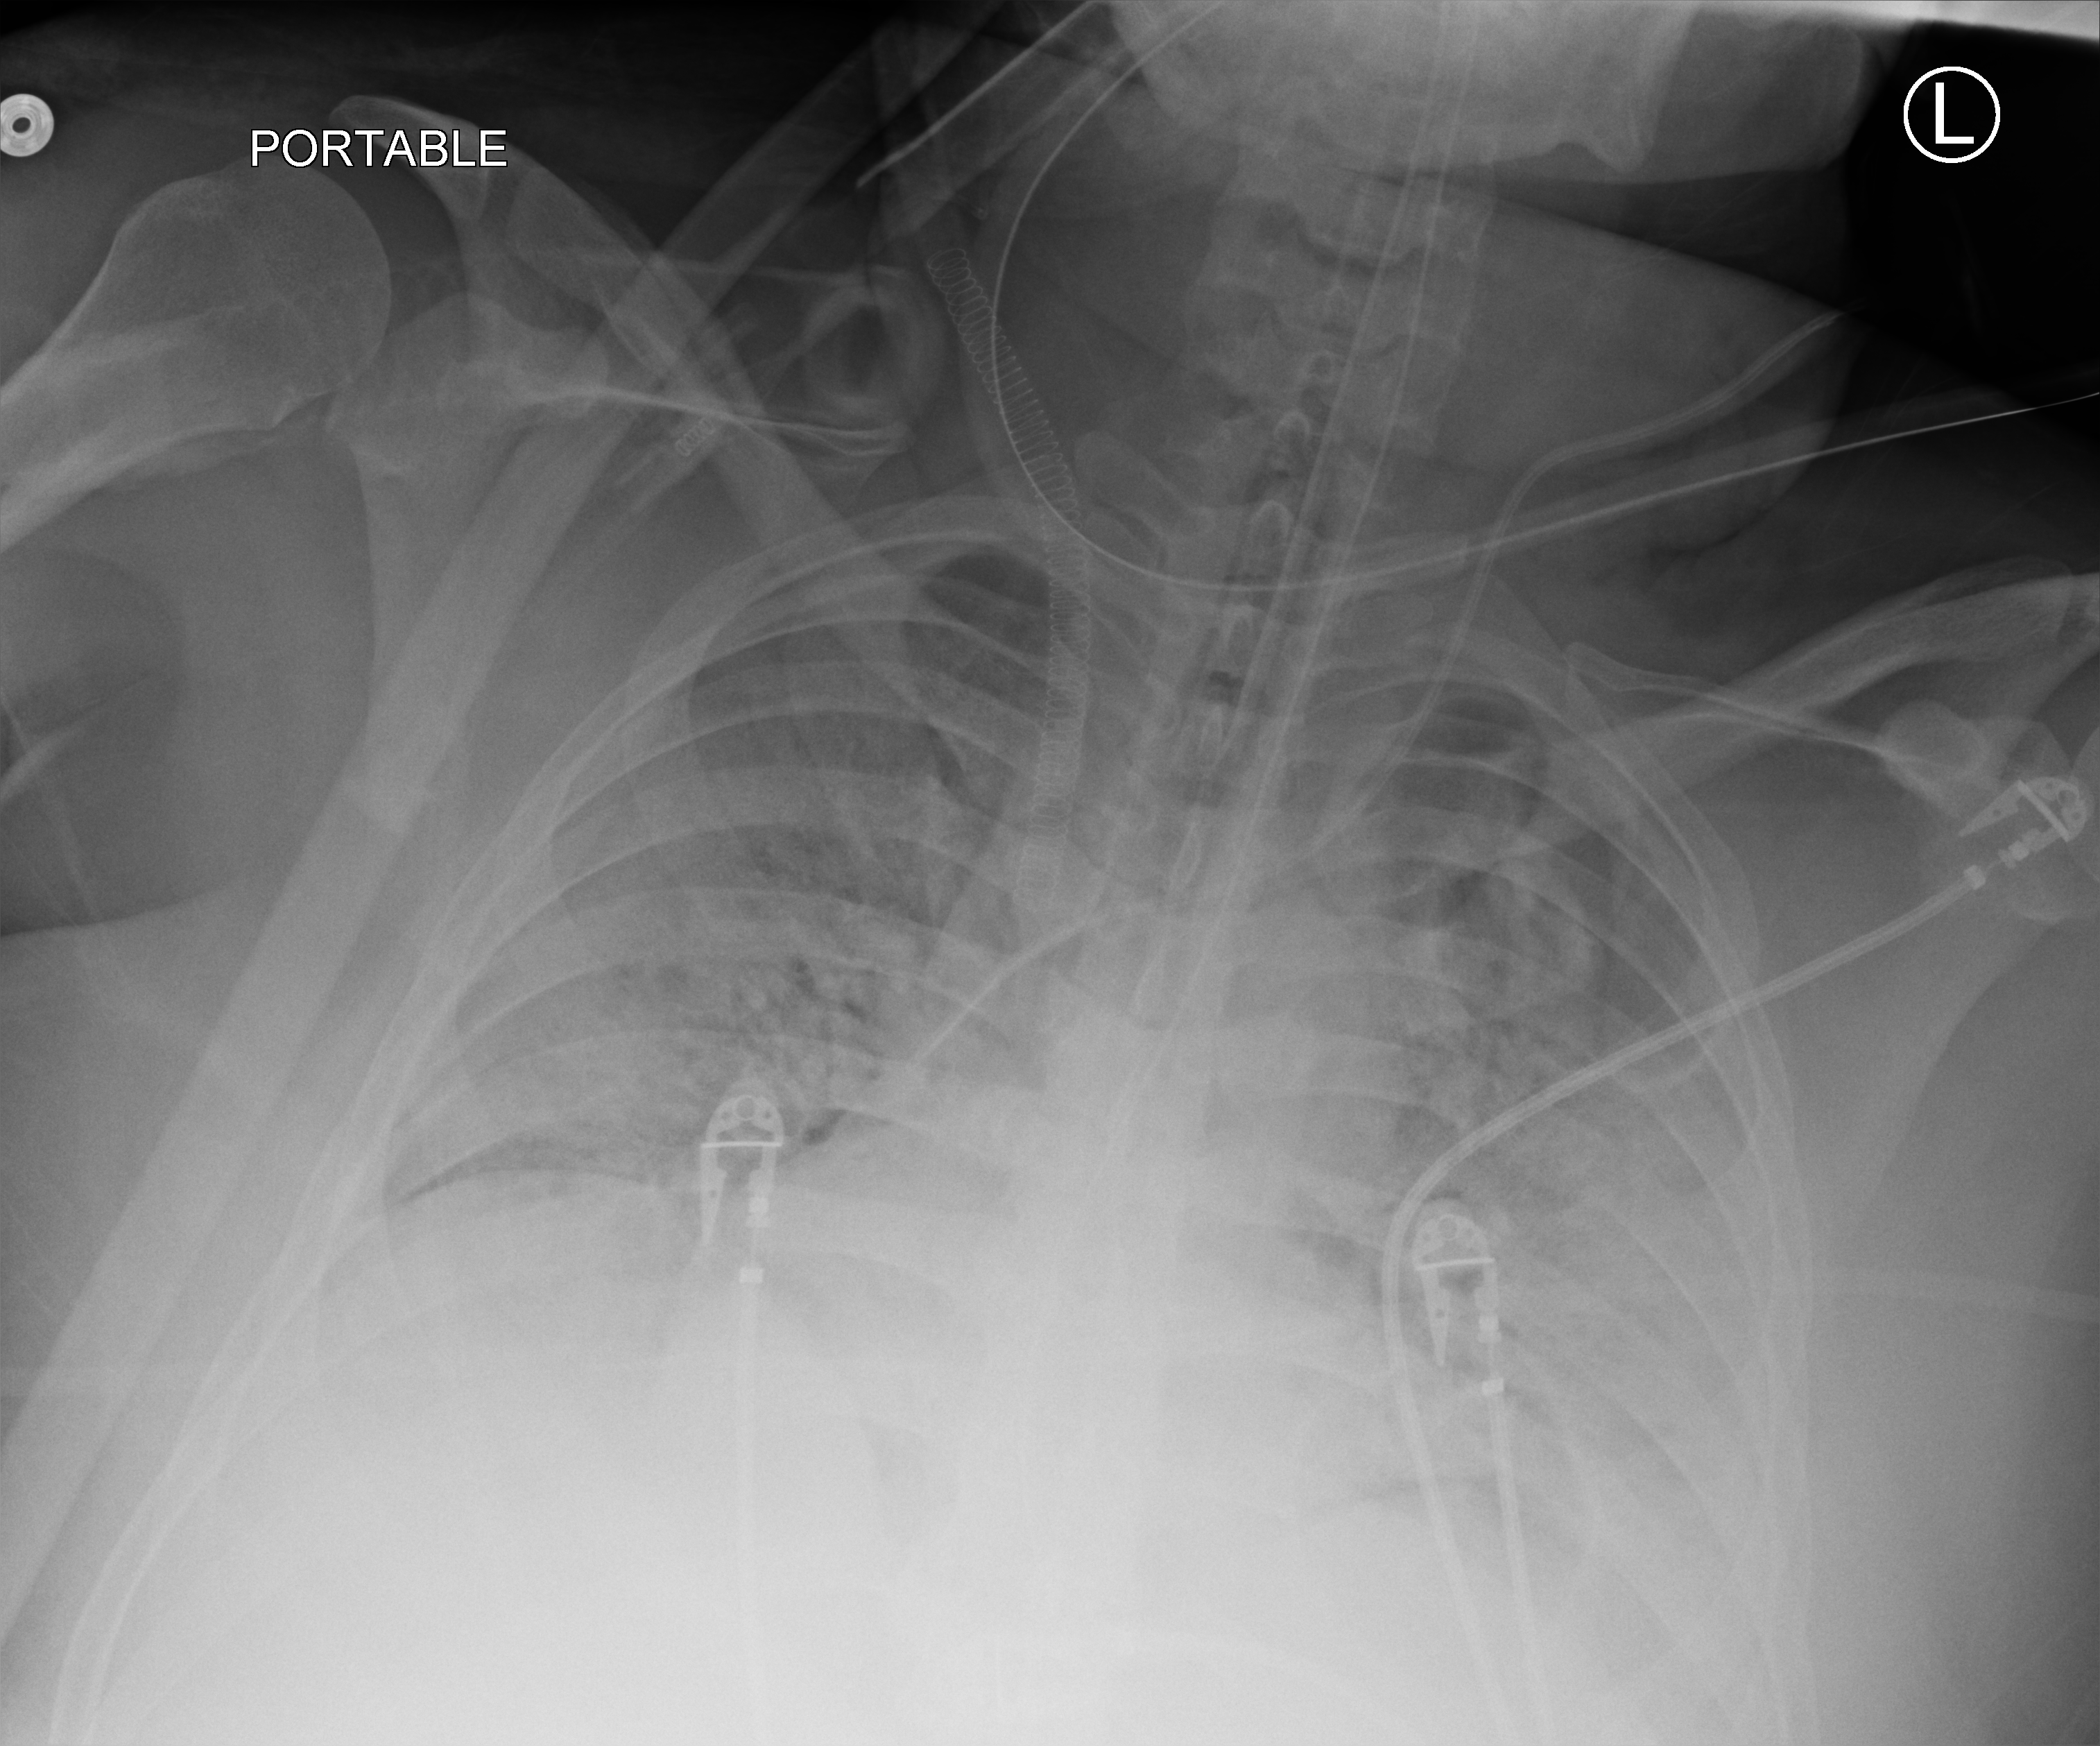
Bedside chest radiograph (computed radiography). Patient hospitalised with COVID-19, aged 18–59 years.
From the hospital-stay record, not from the radiograph (when in the stay this image was taken is not recorded): admitted to intensive care during this hospital stay: yes; mechanically ventilated during this hospital stay: yes.